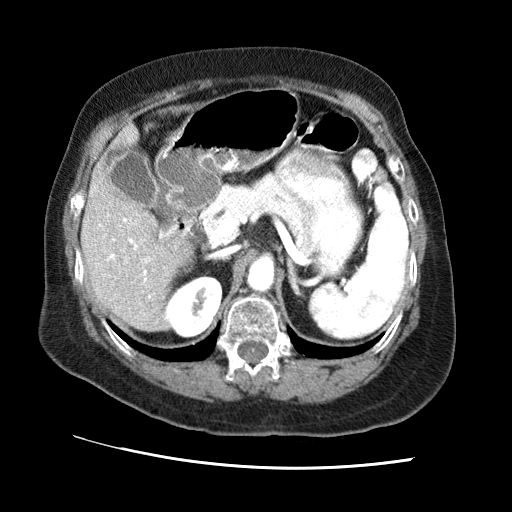
Contrast-enhanced abdominal CT (liver protocol), one axial slice. Slice 32 of 65 in the series (ordered by position). Soft-tissue window (W 400 / L 40 HU). 2.5 mm slice thickness. 512 × 512 image matrix. Case-level facts recorded for this patient, not image findings: diagnosis: hepatocellular carcinoma (patient treated with transarterial chemoembolisation; whether this scan precedes or follows treatment is not stated here); TNM stage (as recorded): Stage-II; Child-Pugh class: A; tumour nodularity: multinodular; tumour size: 2.5 cm.
Outlined on this slice (semi-automatically segmented with operator editing):
- liver parenchyma outside the tumour (the mass and vessels are separate outlines, so this box may not span the whole liver): bounding box (x1, y1, x2, y2) in pixels: (80, 124, 191, 330)
- liver vessels: (99, 214, 163, 298)